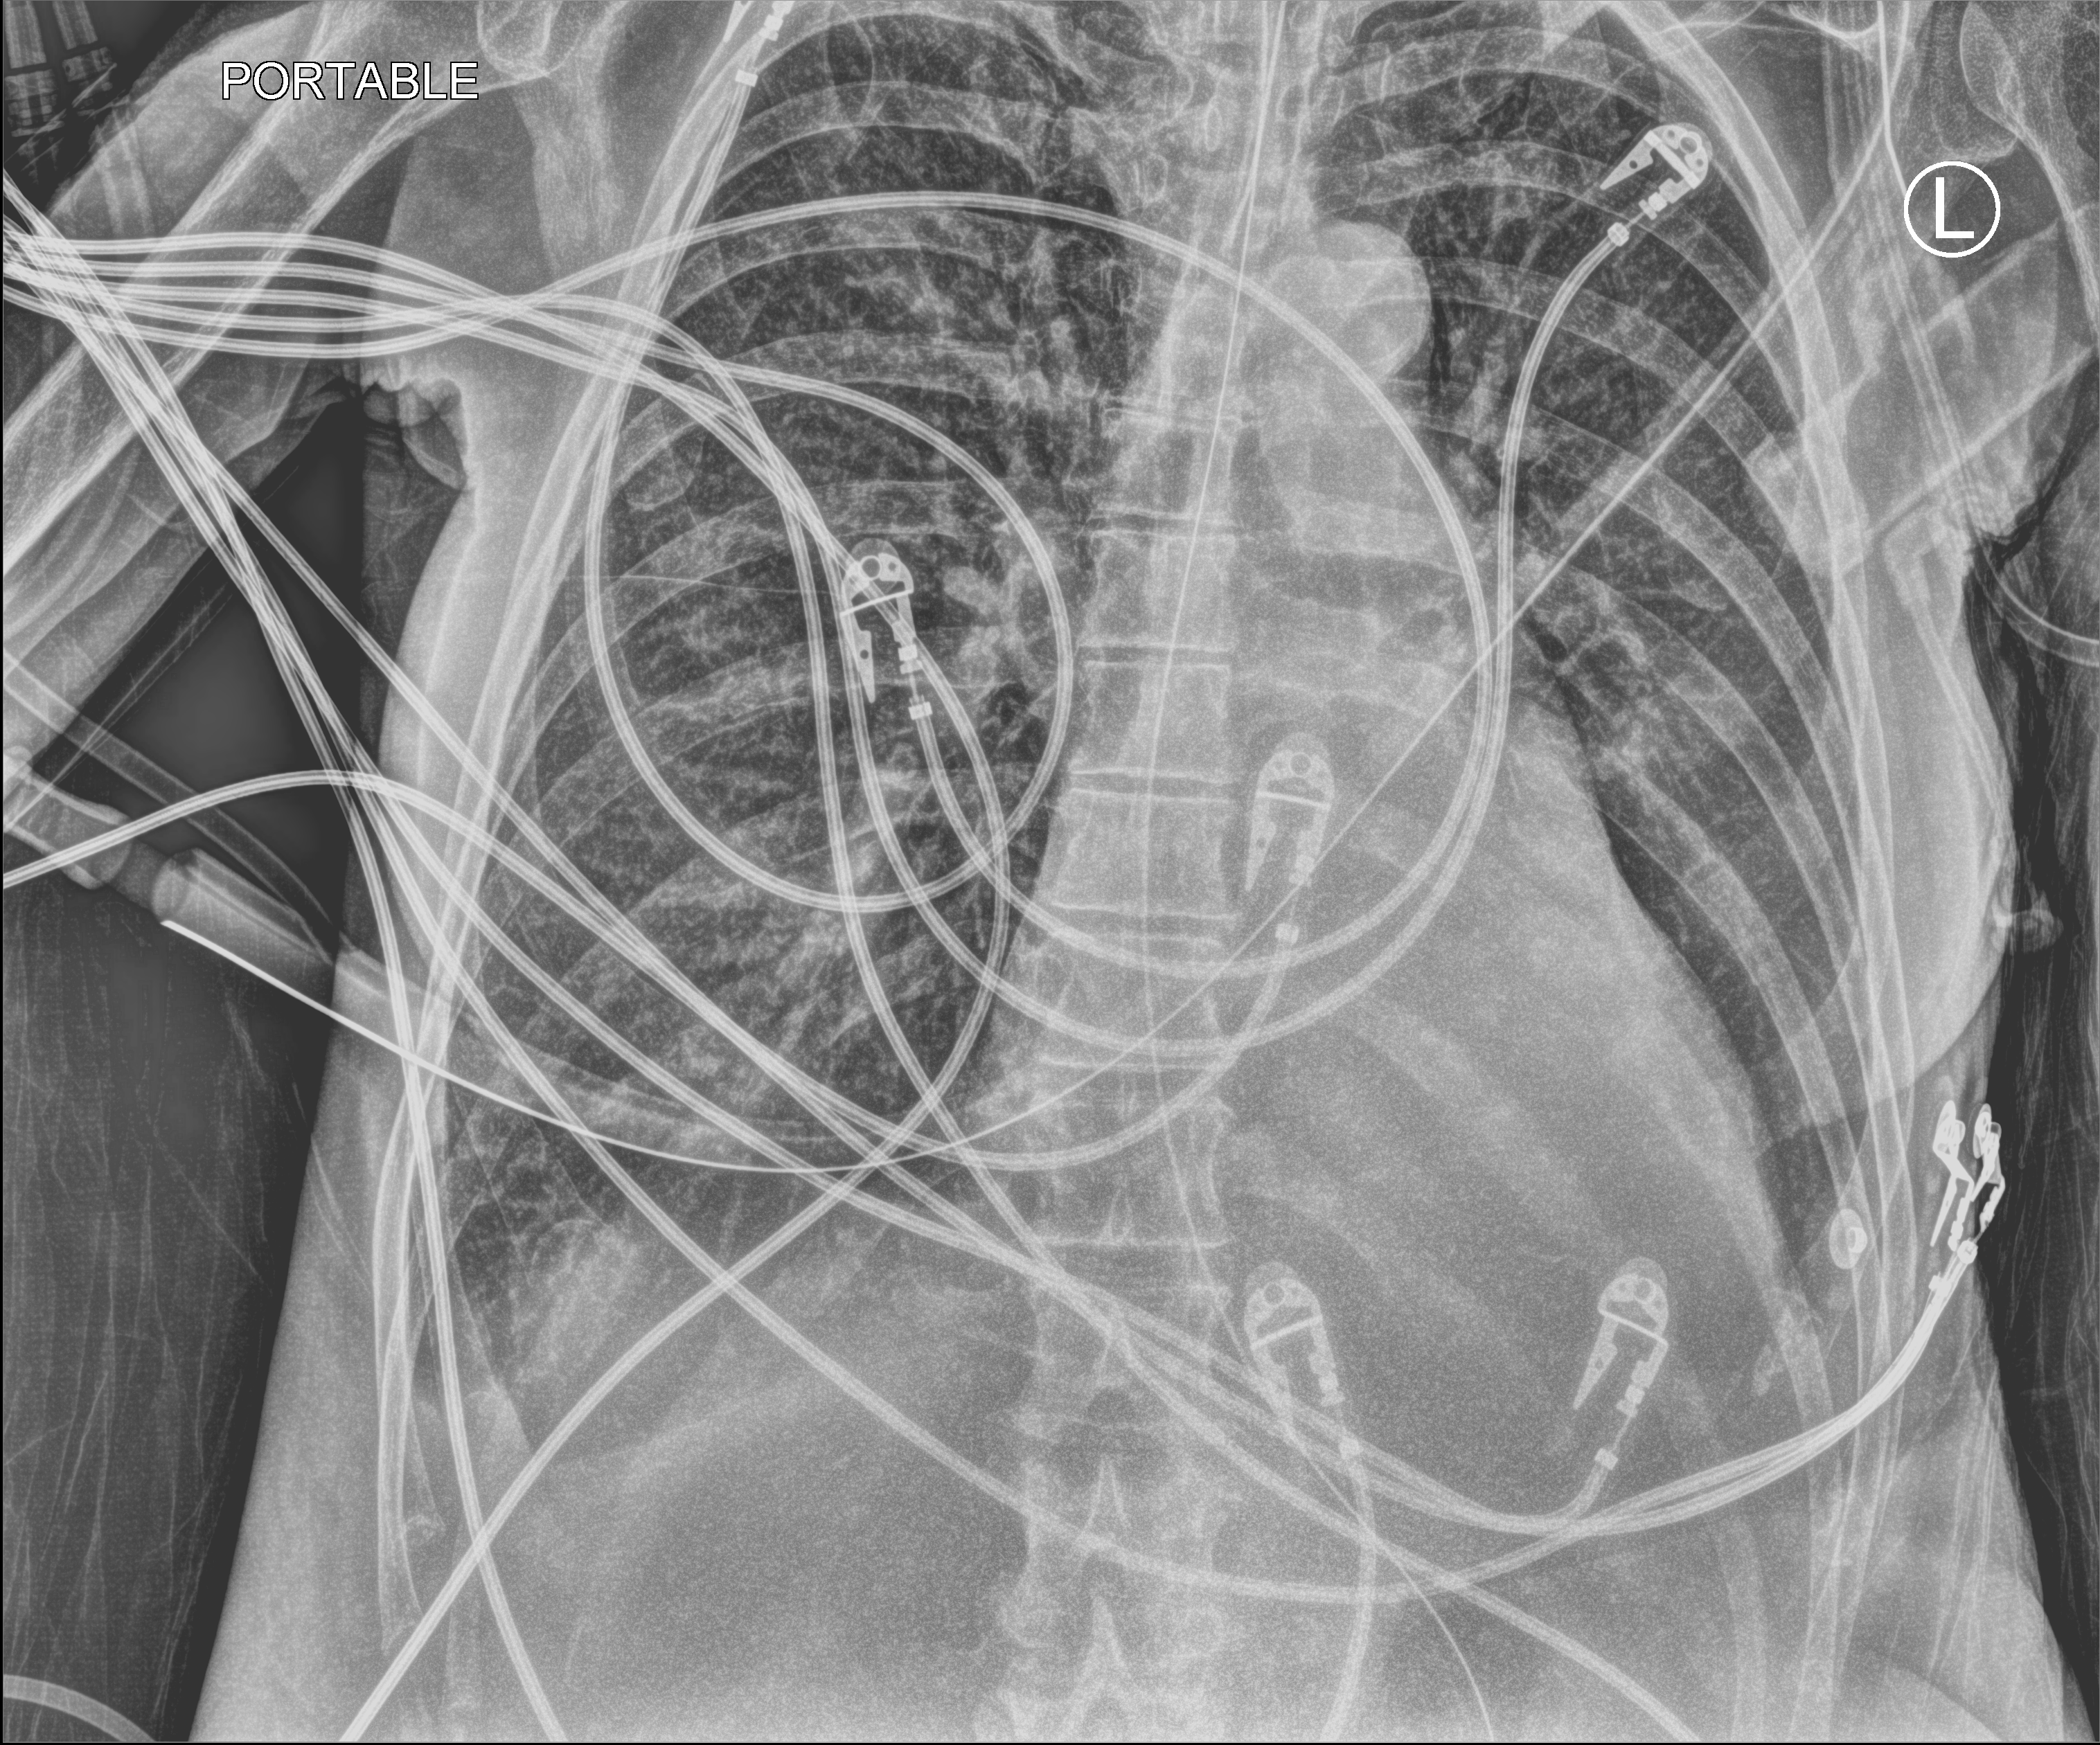
Bedside chest radiograph (computed radiography), anteroposterior (AP) projection. Female patient hospitalised with COVID-19, age 60–74 years.
Admission-level facts for this patient (not findings on this image; timing relative to this image not recorded): admitted to intensive care during this hospital stay: yes; mechanically ventilated during this hospital stay: yes.